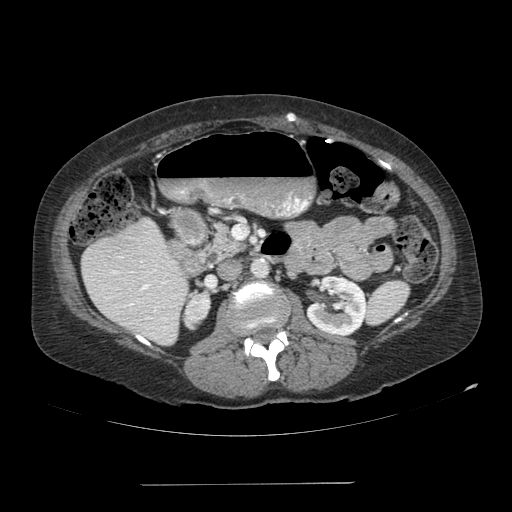
Contrast-enhanced abdominal CT, one axial slice; reconstruction kernel SOFT; soft-tissue window (W 400 / L 40 HU); 2.5 mm slice thickness; 512 × 512 image matrix. Female patient, age 67 years. Case-level facts recorded for this patient, not image findings: diagnosis: adrenocortical carcinoma; tumour side: right adrenal; tumour size at pathology: 9.8 cm; Ki-67 index: 59 %; stage (as recorded): 4.
Structures marked on this image (semi-automatic segmentation, software-assisted and operator-edited):
- mass: bounding box (x1, y1, x2, y2) in pixels: (186, 294, 210, 327)